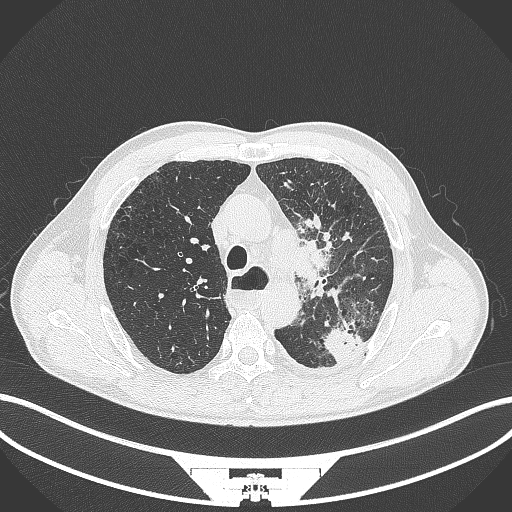
Chest CT, one axial slice; slice 281 of 411 in the series (ordered by position); reconstruction kernel B70f; lung window (W 1500 / L -600 HU); 512 × 512 image matrix, field of view 400 × 400 mm. Patient: male, 57 years. From the clinical record (not read from this slice): clinical TNM (as recorded): T2a N1 M0.
Outlined on this slice (rectangle marked by the reading radiologist):
- lung tumour (recorded histology: squamous cell carcinoma): bounding box [x1, y1, x2, y2] px = [290, 232, 332, 287]